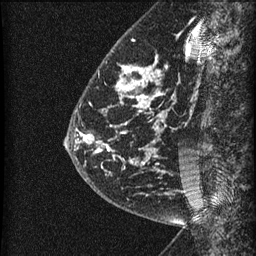
Breast MRI (dynamic contrast-enhanced), one sagittal slice; slice 17 of 60 in the series (ordered by position); dynamic contrast-enhanced series, image 2 of 3 at this slice position (ordered by acquisition); 1.5 T; TE 4.2 ms, TR 22.7 ms; 1.5 mm slice thickness; 256 × 256 image matrix. Patient: female, 48 years. From the clinical record (not read from this slice): setting: breast cancer imaged before/during neoadjuvant chemotherapy; receptor status: triple-negative.
Structures marked on this image (semi-automatically segmented with operator editing):
- analysis volume of interest (the breast-tissue region the enhancement analysis was run in; not a lesion): bounding box <81,23,186,202> (left, top, right, bottom; pixels)
- tumour enhancement mask (voxels above the 90 % enhancement threshold inside the analysis volume of interest): <81,64,162,164>